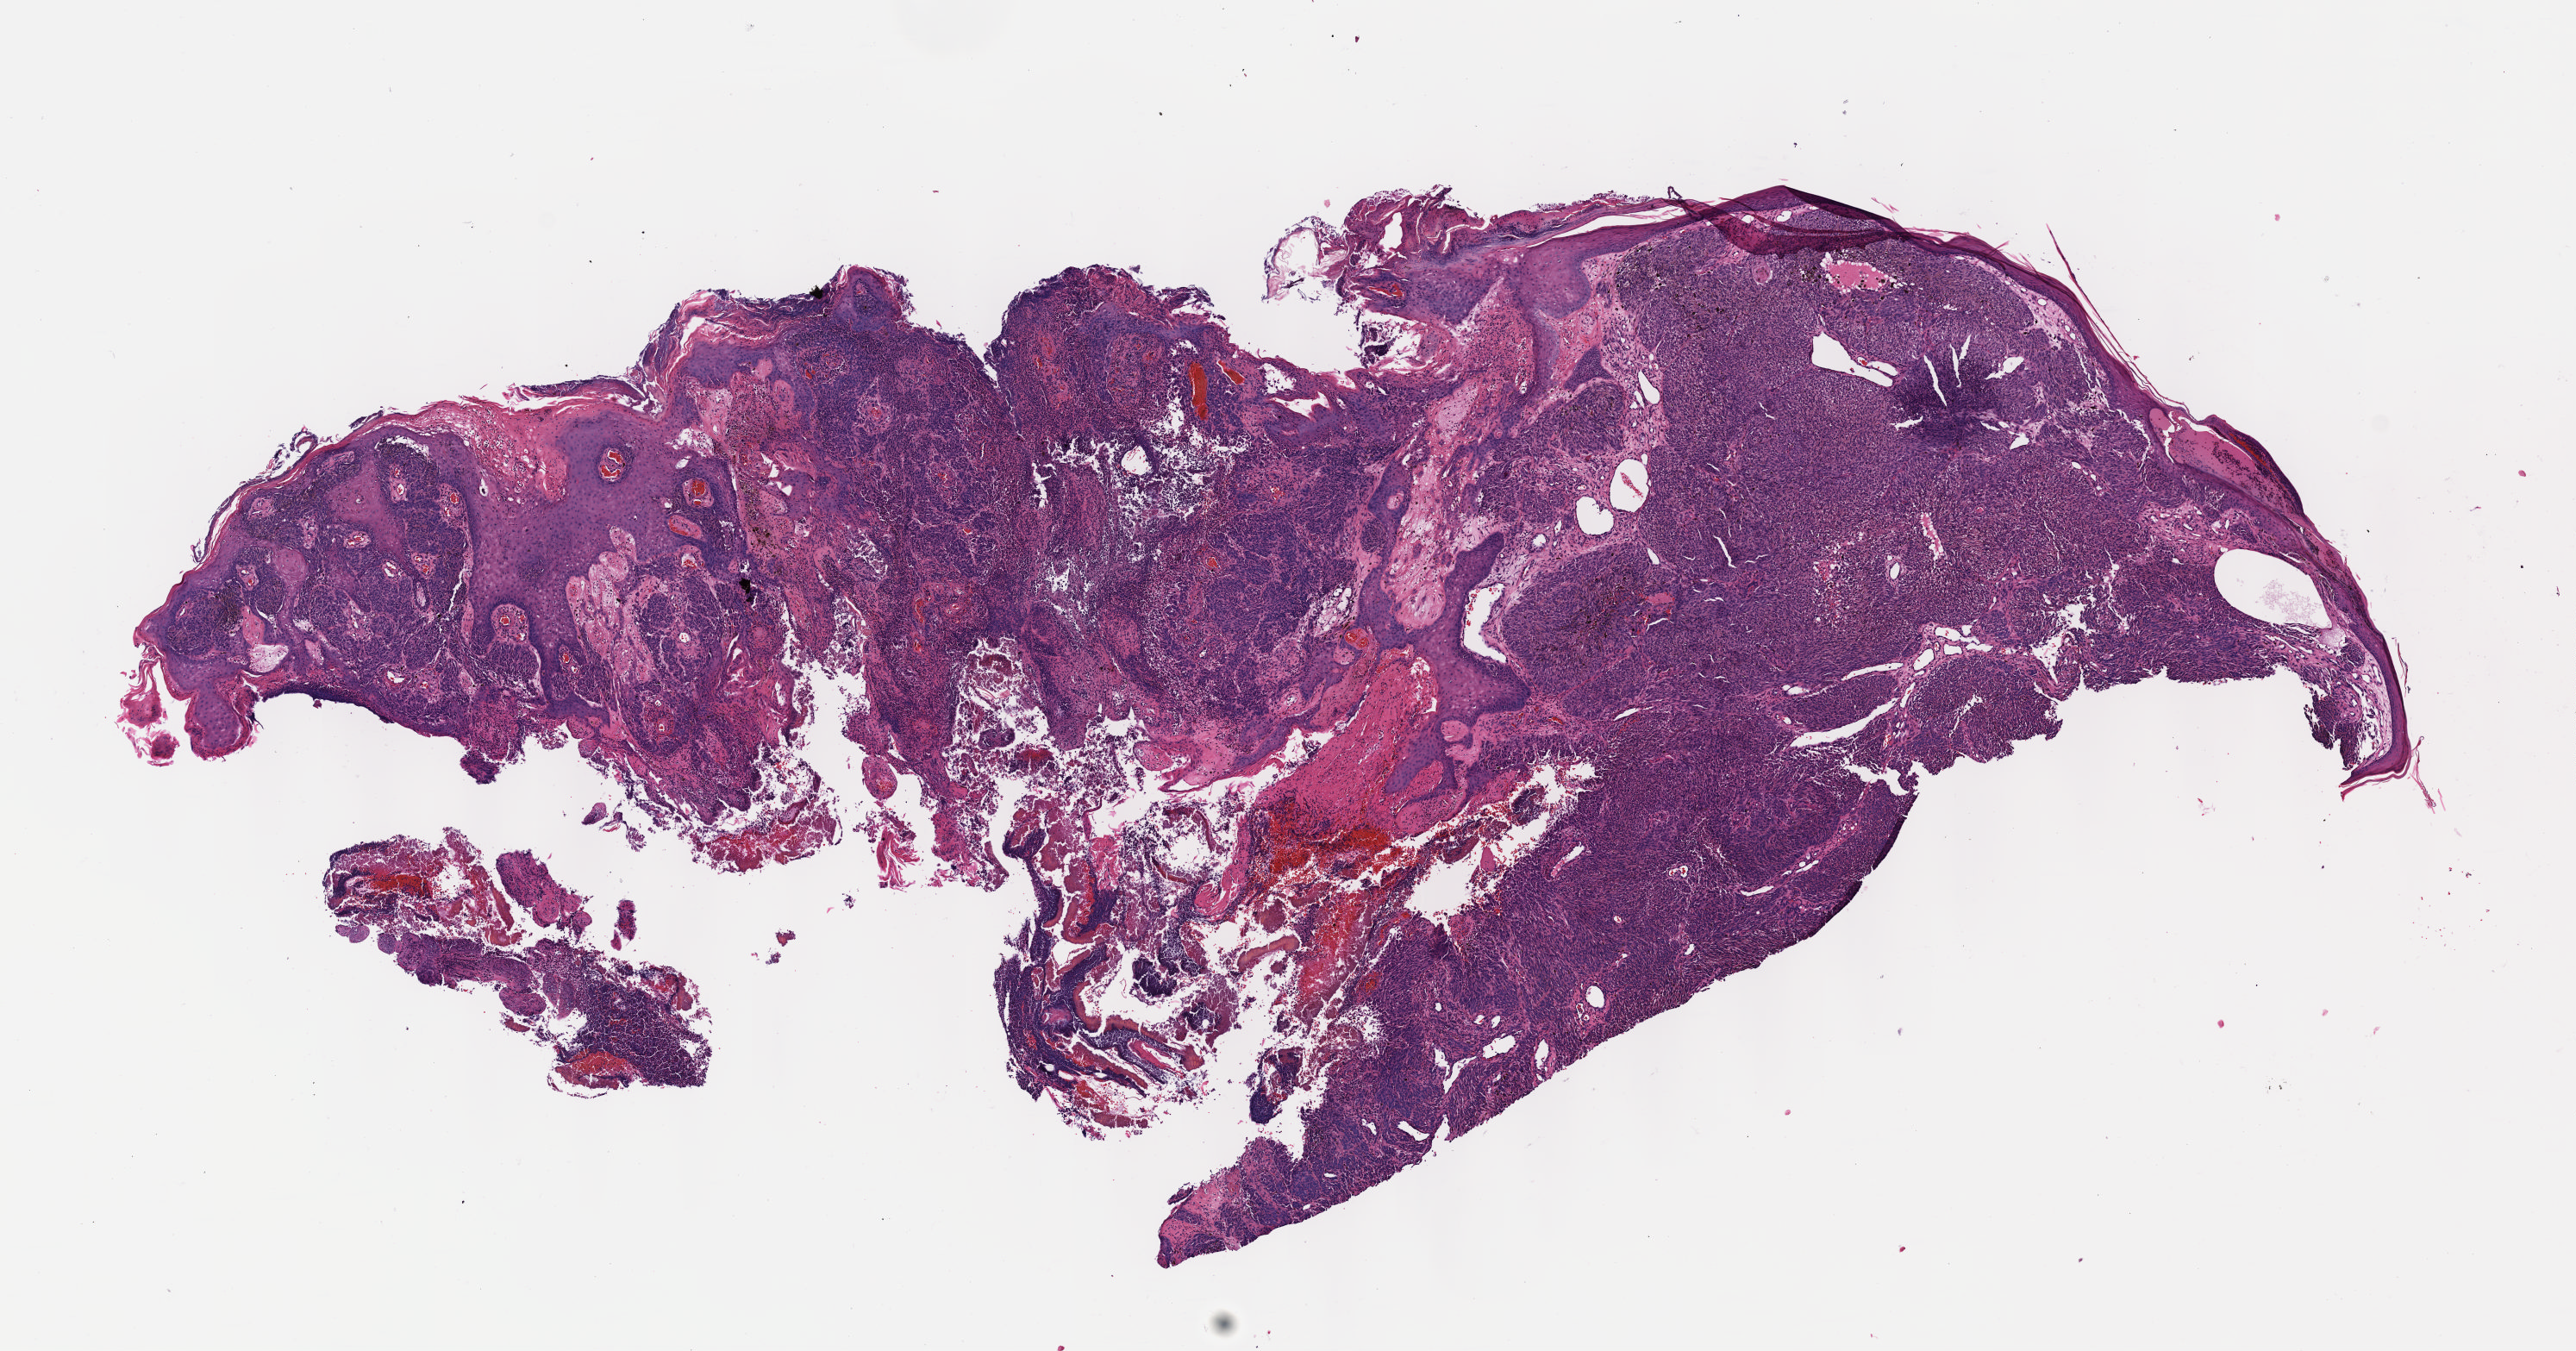
Whole-slide histology image, H&E — whole scanned area (about 12.1 x 6.3 mm, slide scanned at 40x) shown as a low-resolution overview; formalin-fixed paraffin-embedded (FFPE) diagnostic section; primary tumour sample from the skin. Female, age 46 years at initial diagnosis.
Histologic diagnosis: Malignant melanoma, NOS. AJCC pathologic stage: IIC.